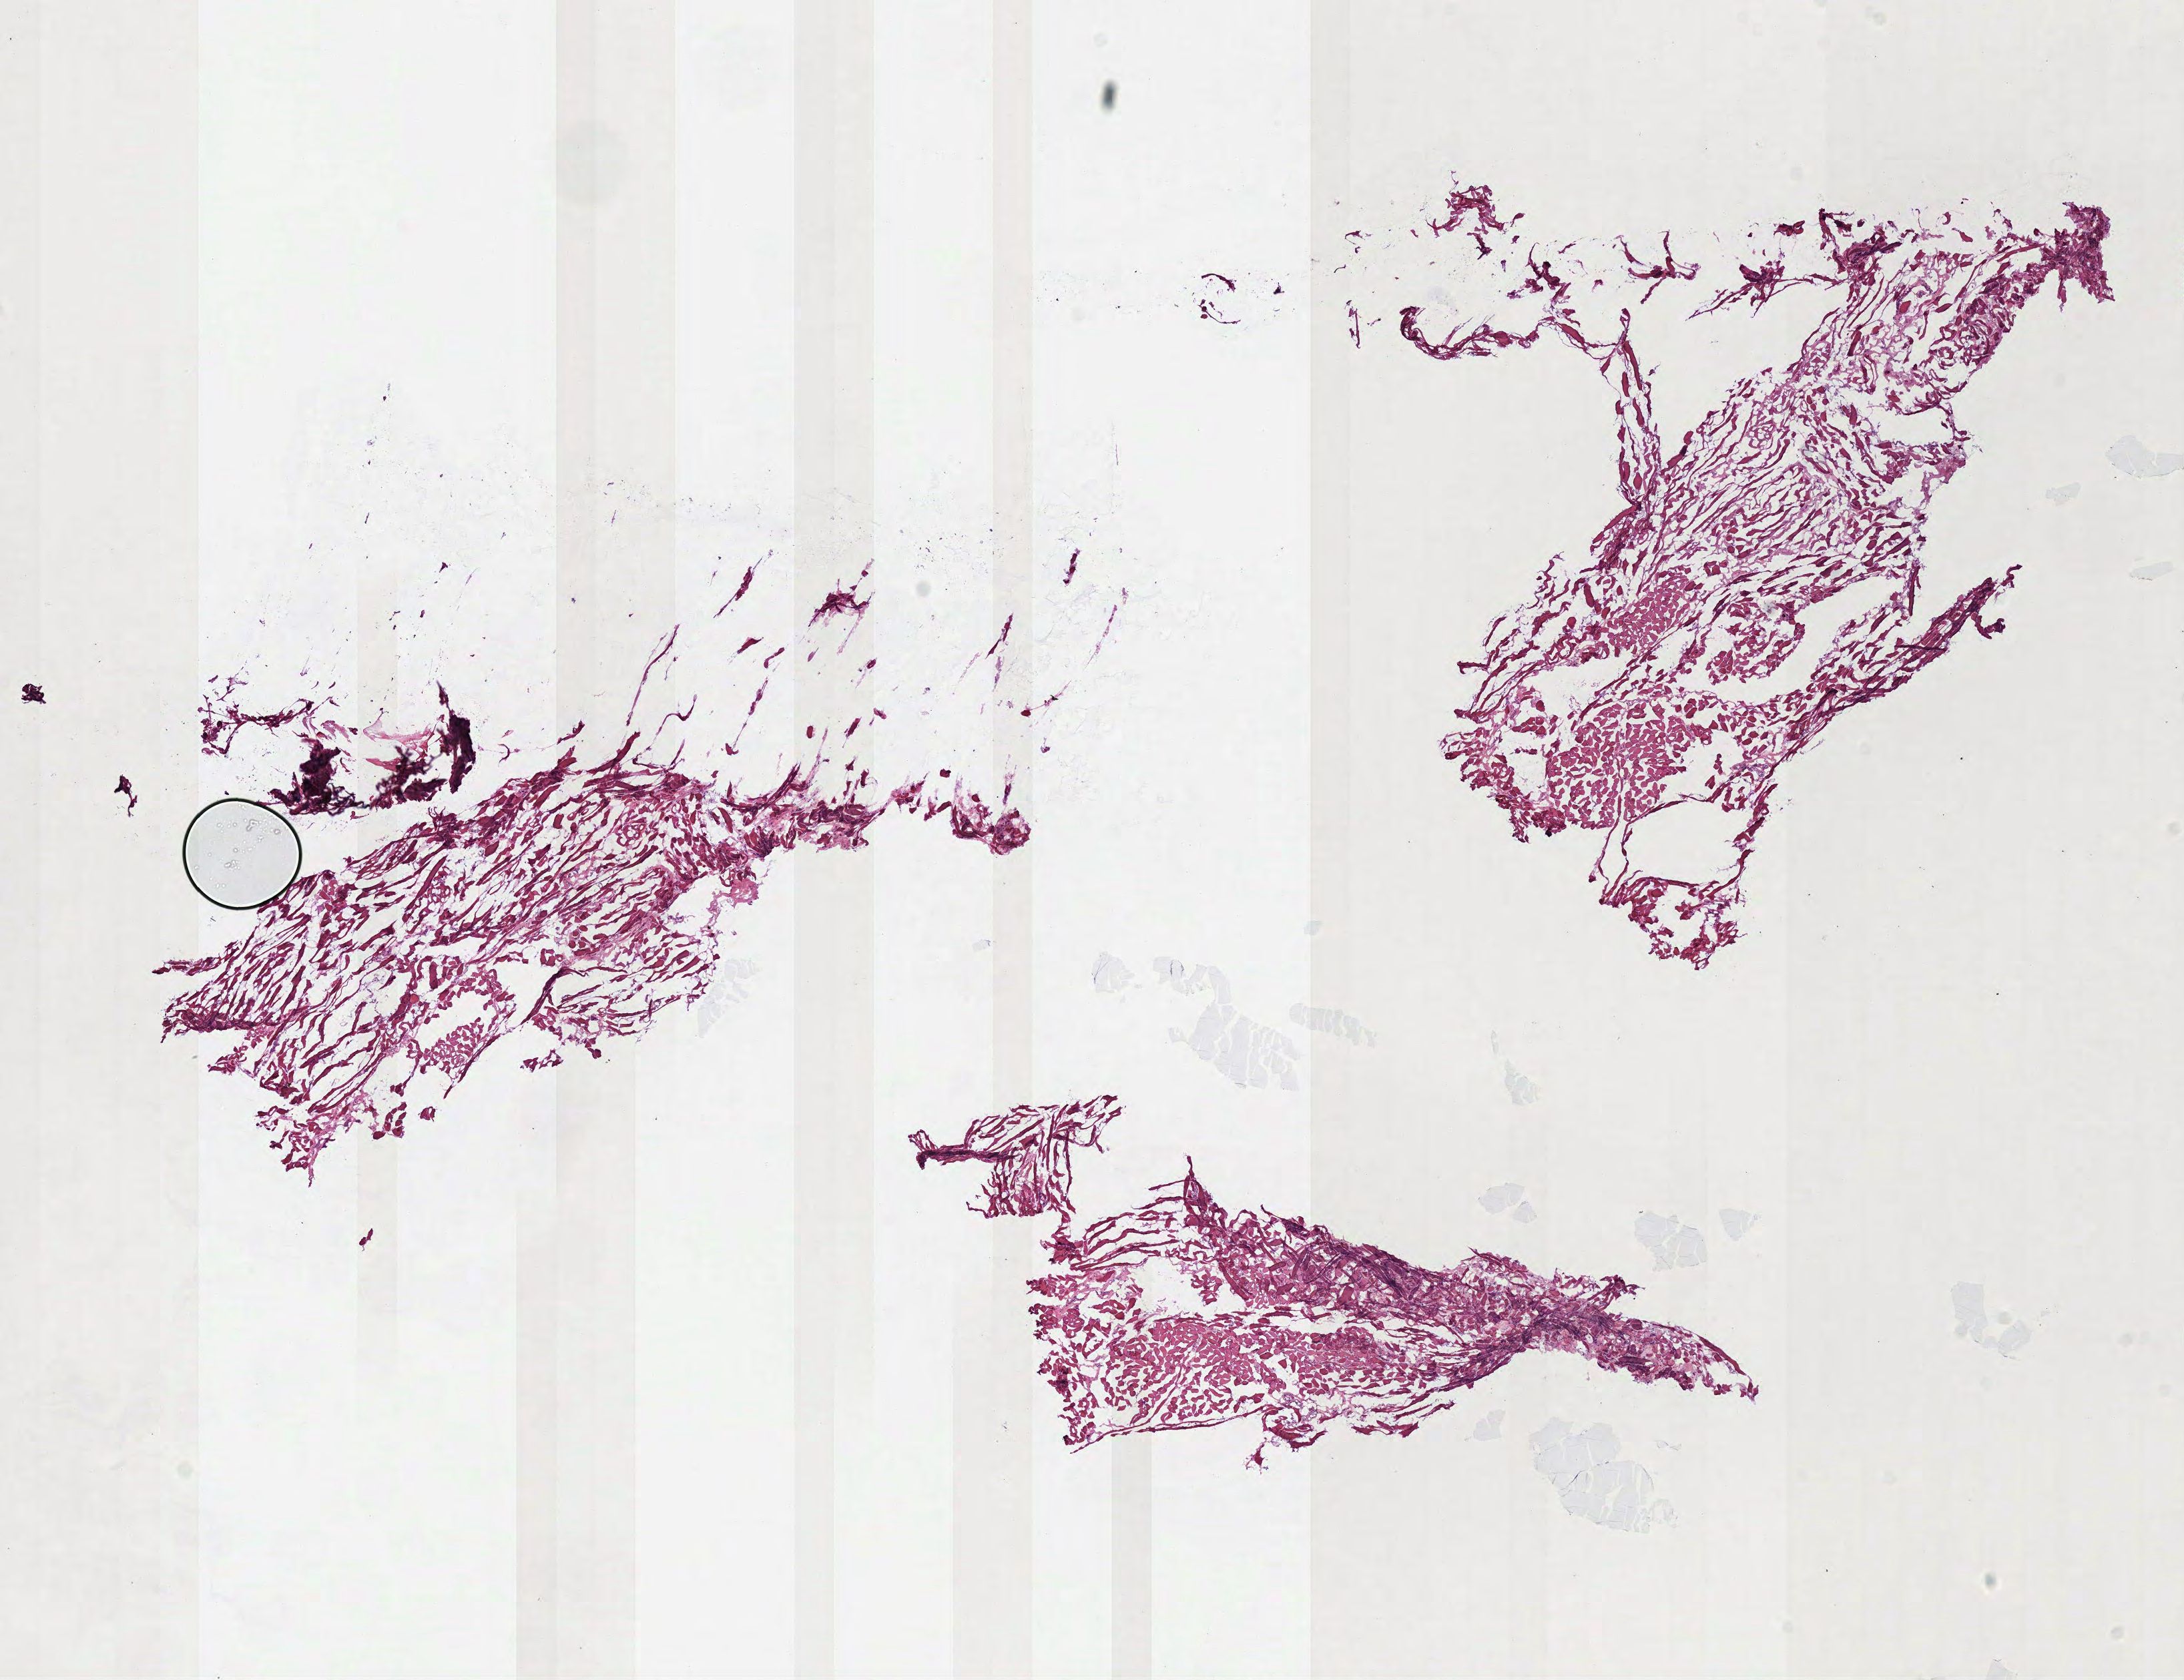
Digitized Hematoxylin and eosin (H&E) stained tissue section (whole slide), low-resolution overview of the scanned area, about 12.9 x 9.9 mm (slide scanned at 40x), frozen section from the top of the tissue portion, solid tissue normal (non-tumour tissue) sample from the head and neck. Patient: male, age at initial diagnosis 48 years.
- this section: solid tissue normal (non-tumour) sample from the same patient
- patient diagnosis: Squamous cell carcinoma, NOS (tongue, NOS)